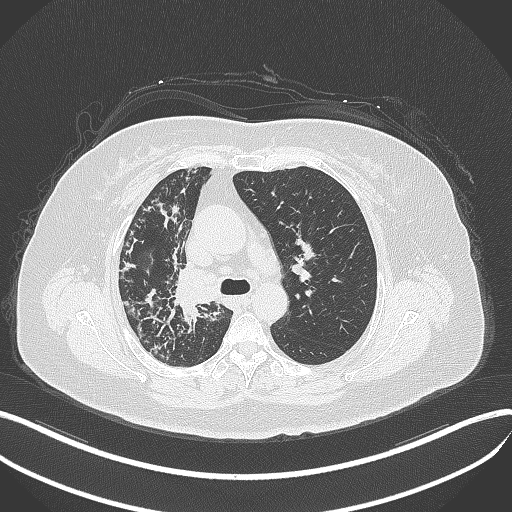
Chest CT, one axial slice; position 241 of 376 along the scan axis; 120 kVp; lung window (W 1500 / L -600 HU); 512 × 512 image matrix, field of view 400 × 400 mm. Patient: female, 60 years. From the clinical record (not read from this slice): clinical TNM (as recorded): T1c N0 M0; histopathological grade: G1-G2.
Structures marked on this image (bounding box drawn by a radiologist):
- lung tumour (recorded histology: squamous cell carcinoma): bounding box (x1, y1, x2, y2) in pixels: (171, 265, 232, 307)